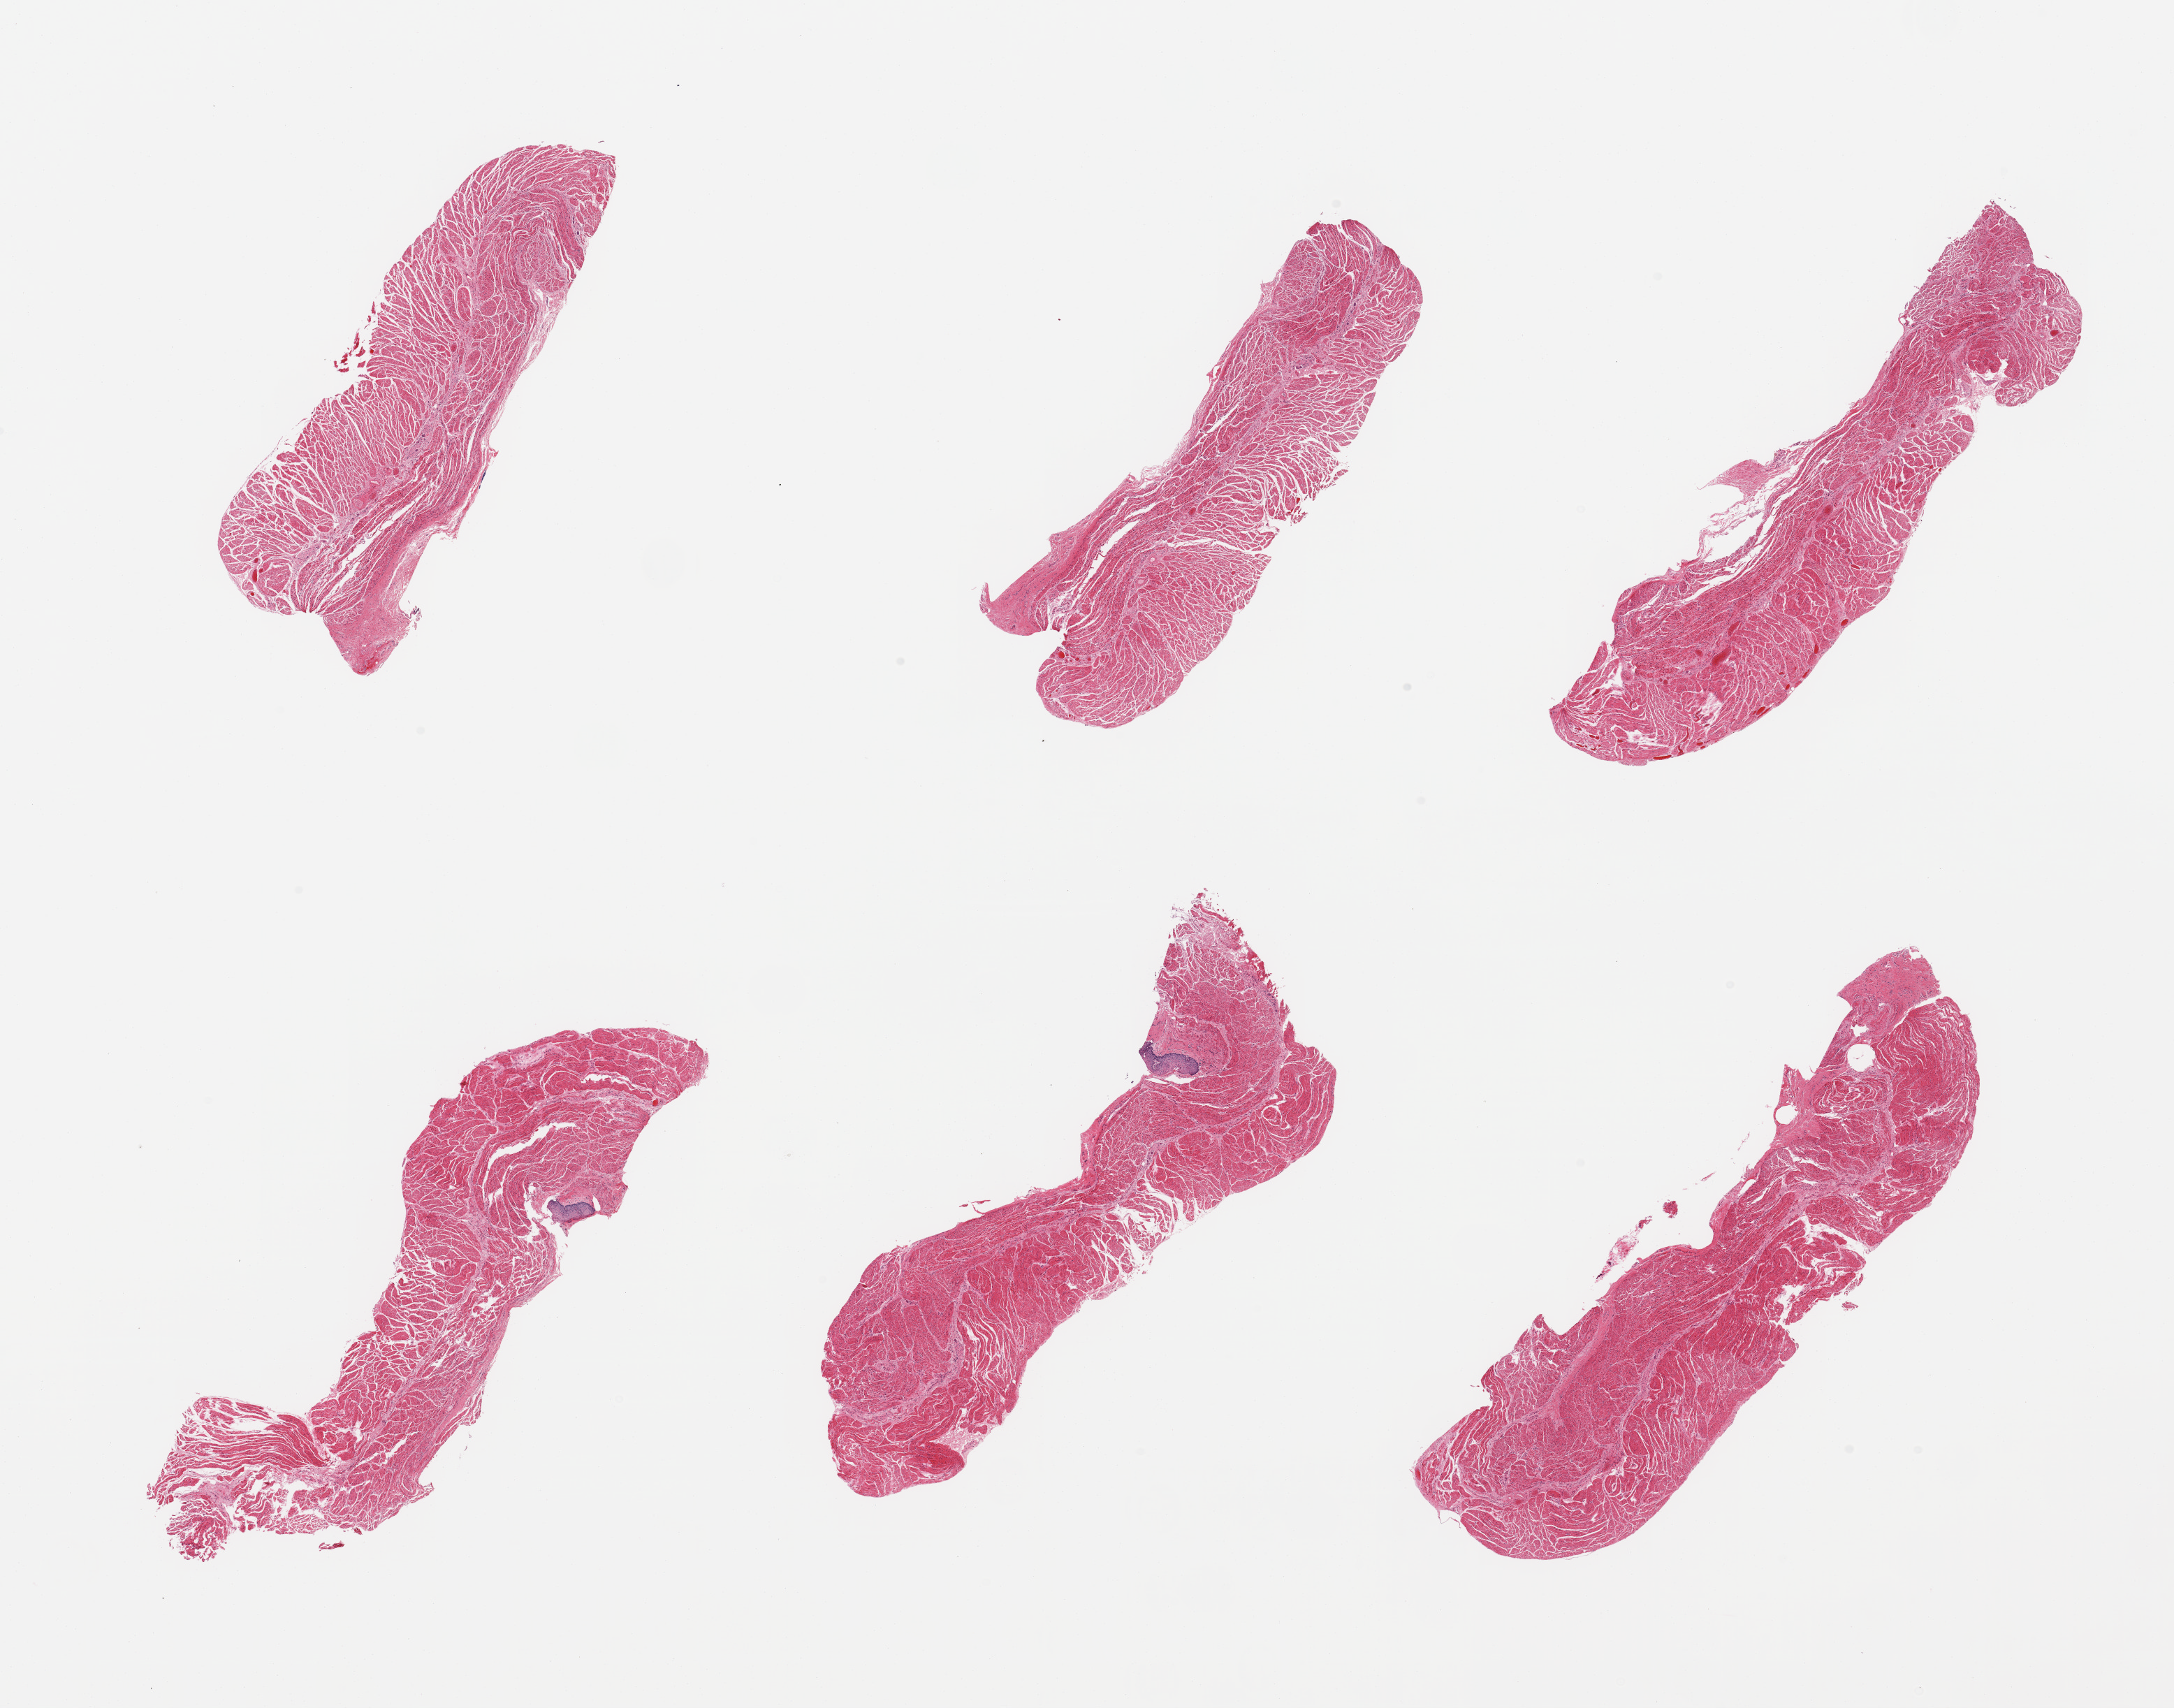
Digitized haematoxylin and eosin-stained section — low-resolution overview of the scanned area, about 24.6 x 19.3 mm (acquisition: 20x scan). PAXgene-fixed, paraffin-embedded tissue. Sampled site (target tissue): esophageal muscle. Donor tissue sample.
Review note (as recorded): 6 pieces, confirmed target muscularis; minute focus of trace squamous mucosa.